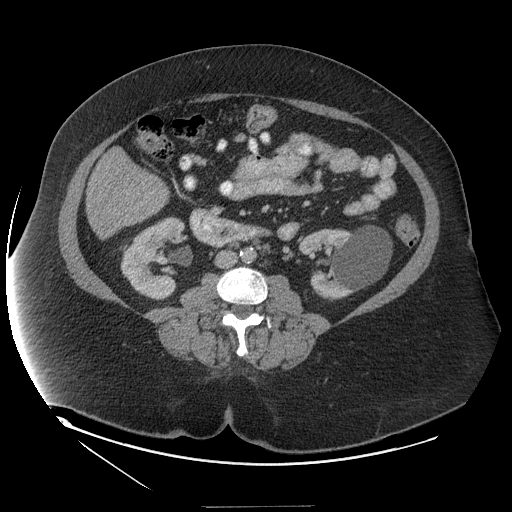
Contrast-enhanced abdominal CT (liver protocol), one axial slice. Slice 33 of 127 in the series (ordered by position). Reconstruction kernel STANDARD. 140 kVp. Soft-tissue window (W 400 / L 40 HU). 512 × 512 image matrix. From the clinical record (not read from this slice): diagnosis: hepatocellular carcinoma (patient treated with transarterial chemoembolisation; whether this scan precedes or follows treatment is not stated here); TNM stage (as recorded): Stage-II; Child-Pugh class: A.
Outlined on this slice (semi-automatically segmented with operator editing):
- liver parenchyma outside the tumour (the mass and vessels are separate outlines, so this box may not span the whole liver): box from (x=86, y=184) to (x=167, y=238) px